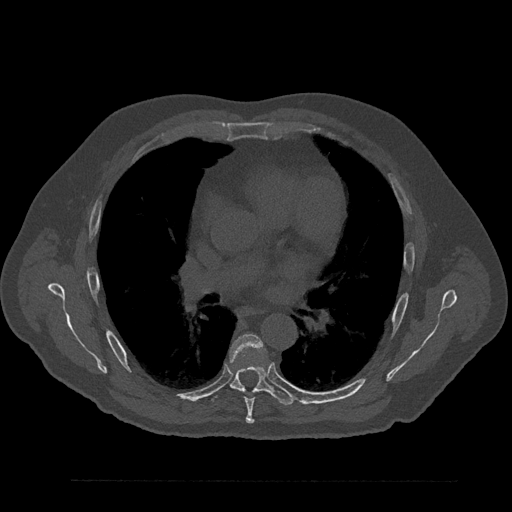
CT including the spine, one axial slice; position 530 of 797 along the scan axis; bone window (W 1800 / L 400 HU); 512 × 512 image matrix, field of view 430 × 430 mm. Male patient, age 61 years. Case-level facts recorded for this patient, not image findings: primary cancer: prostate.
Outlined on this slice (semi-automatically segmented with operator editing):
- T6 vertebra: bounding box [x1, y1, x2, y2] px = [230, 335, 266, 424]
- T7 vertebra: [211, 355, 294, 405]